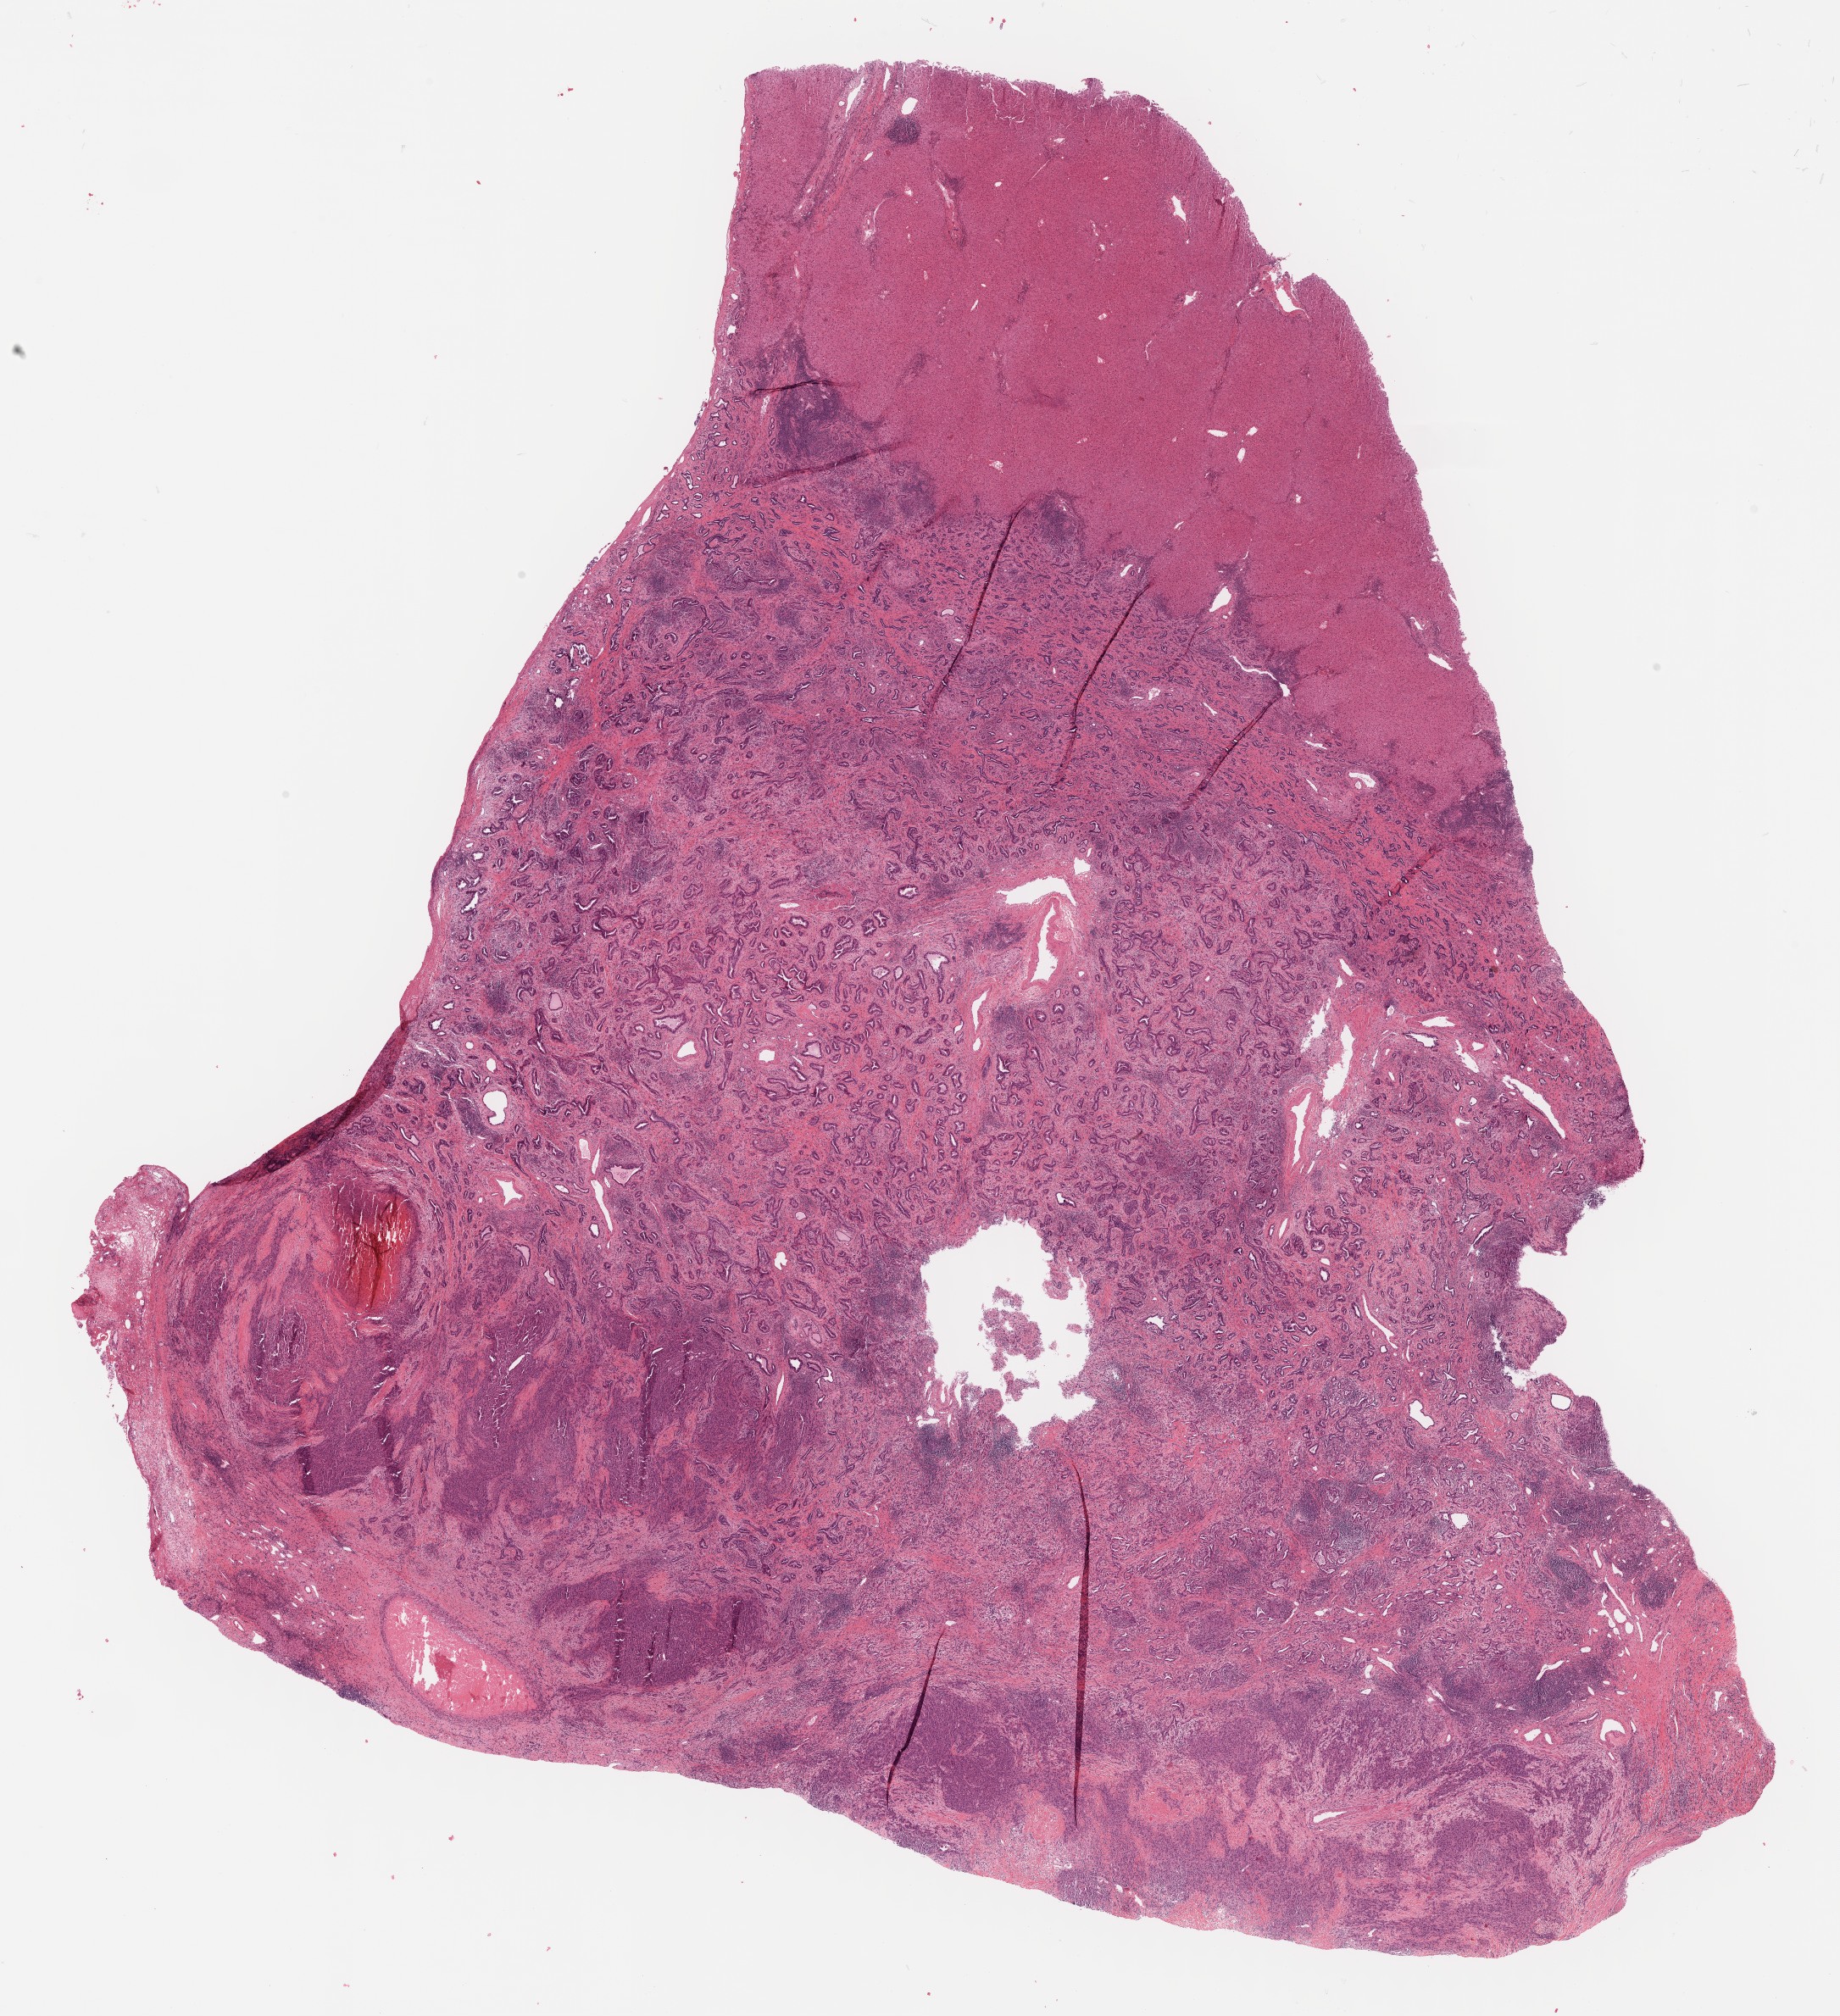
Digitized H&E tissue section (whole slide), low-resolution overview of the scanned area, about 17.6 x 19.3 mm (slide scanned at 40x); formalin-fixed paraffin-embedded (FFPE) diagnostic section; primary tumour sample from the bile duct. Female patient; age at initial diagnosis 77 years.
Pathologic diagnosis: Cholangiocarcinoma.